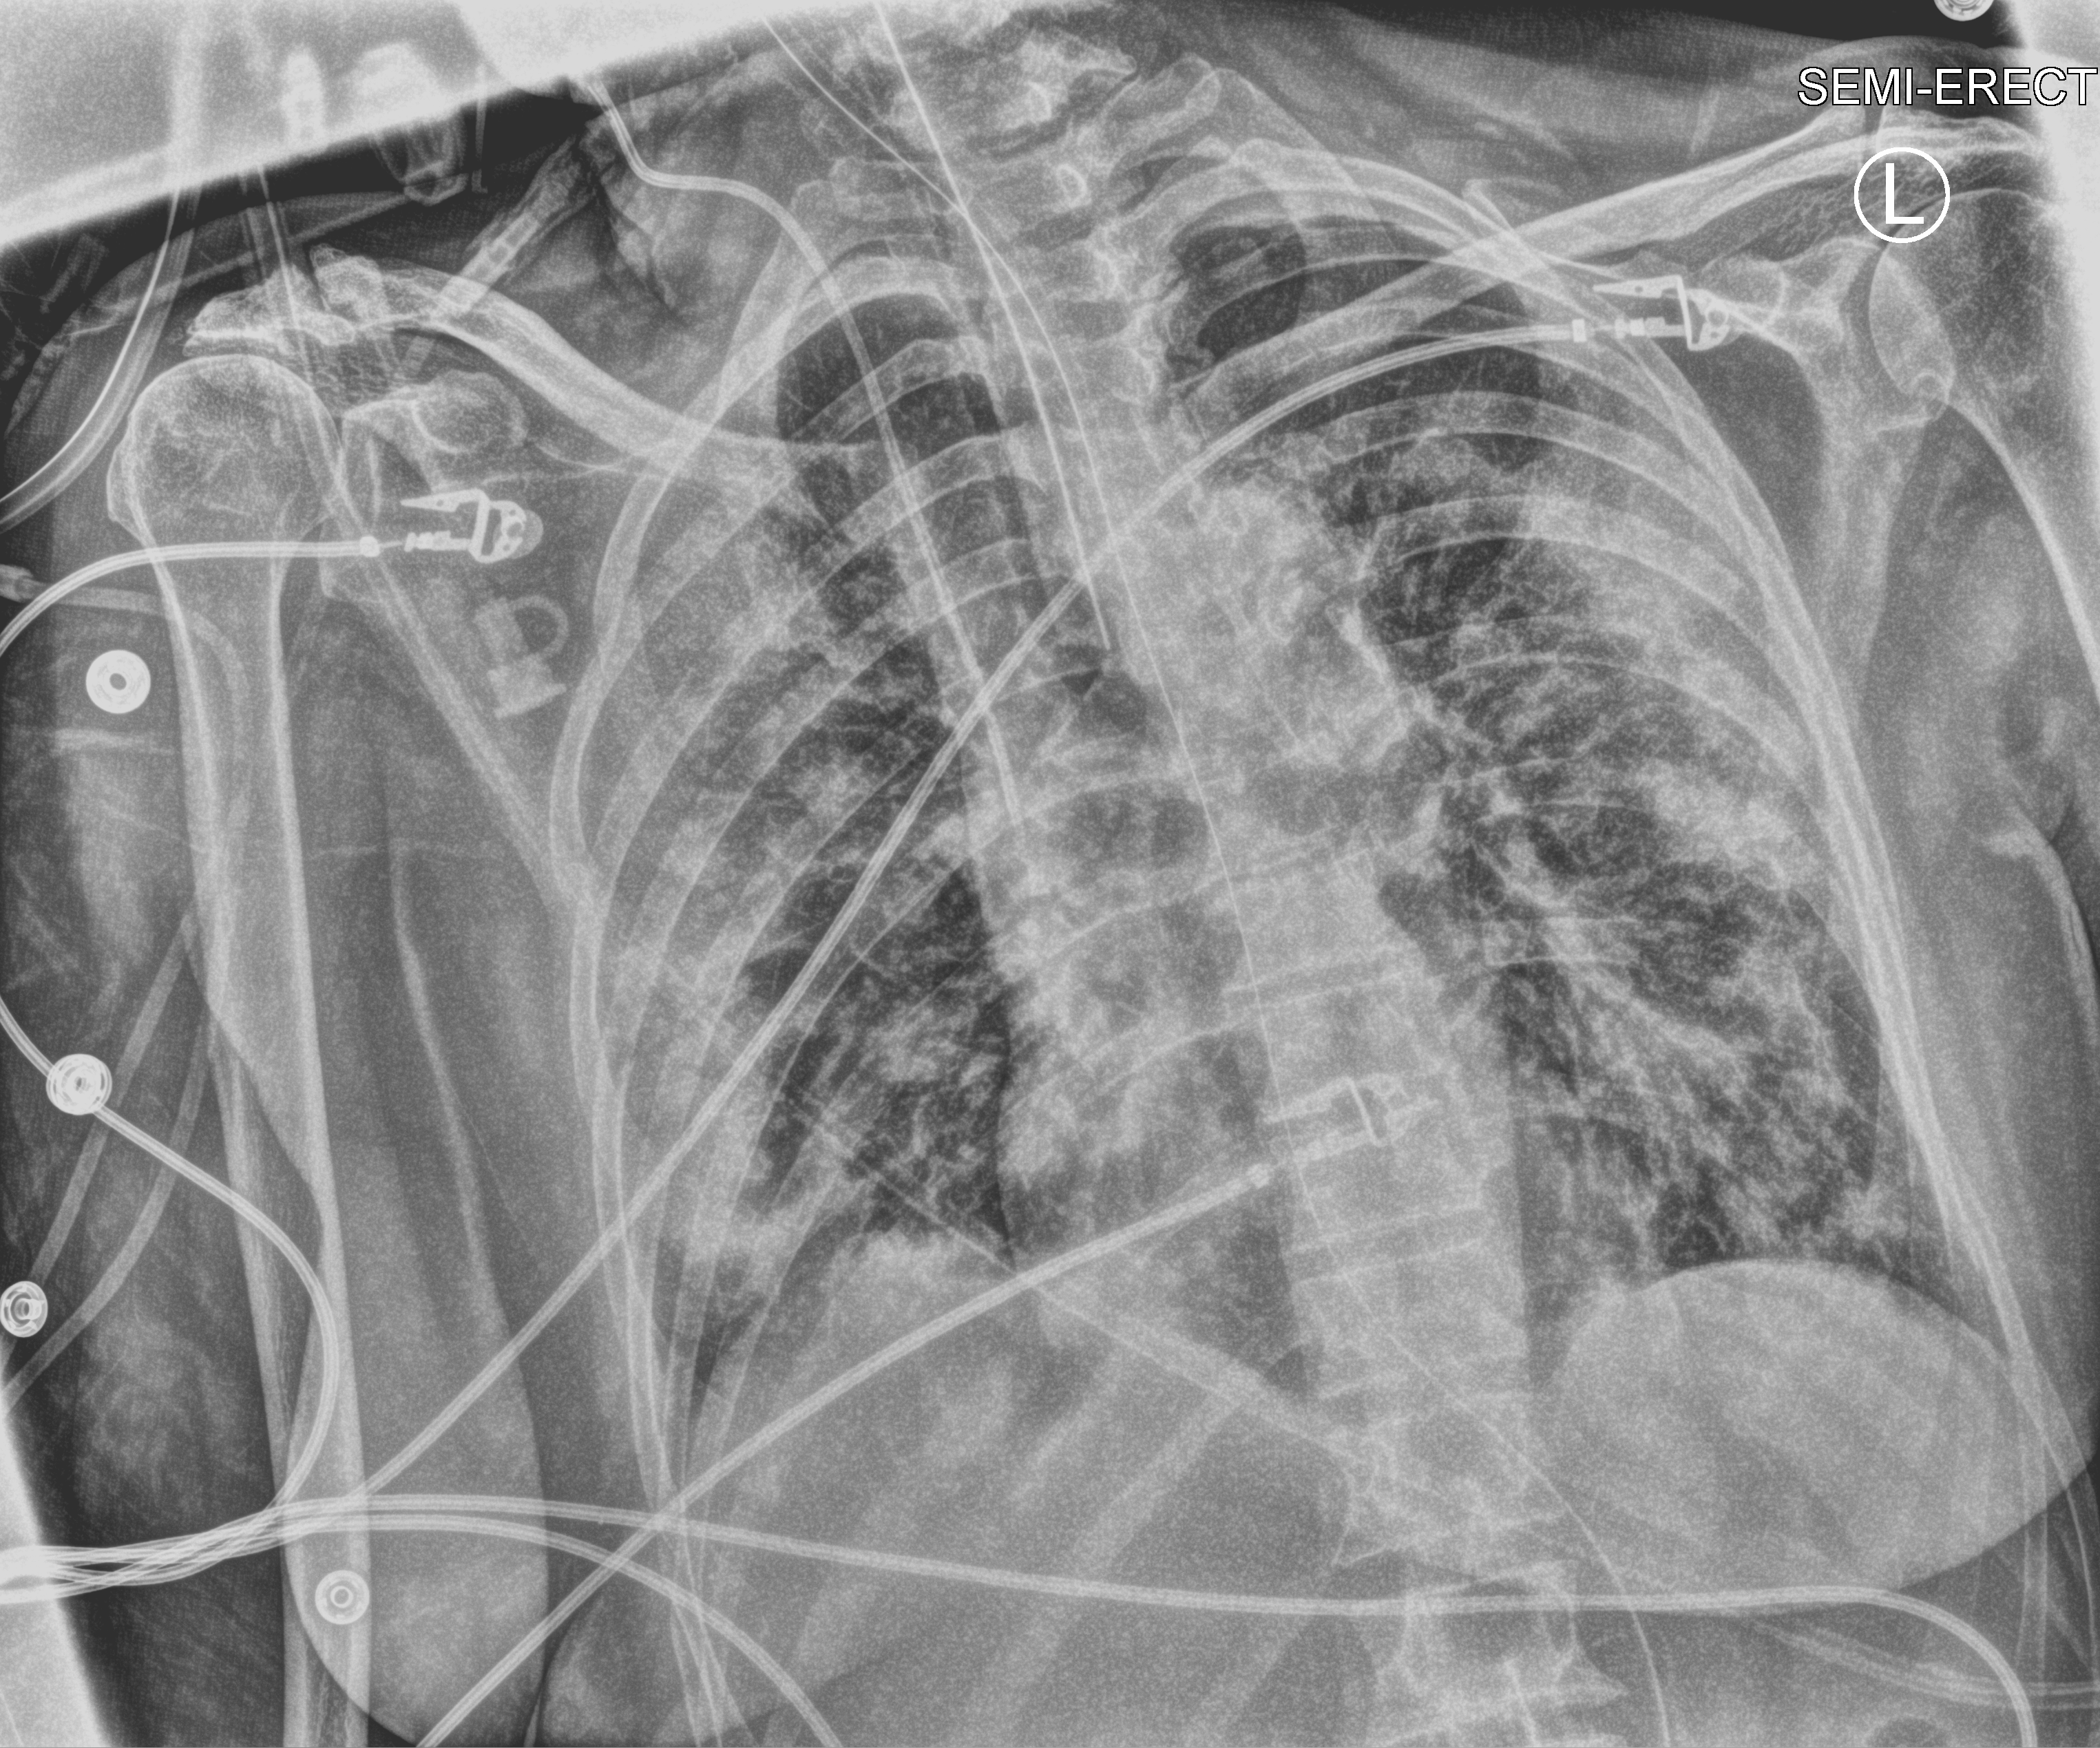
Bedside chest radiograph (computed radiography), anteroposterior (AP) projection. Female patient hospitalised with COVID-19, age 60–74 years.
Hospital-stay facts (about this admission, not read from this image; timing relative to this image not recorded): other chronic lung disease (admission record): no.